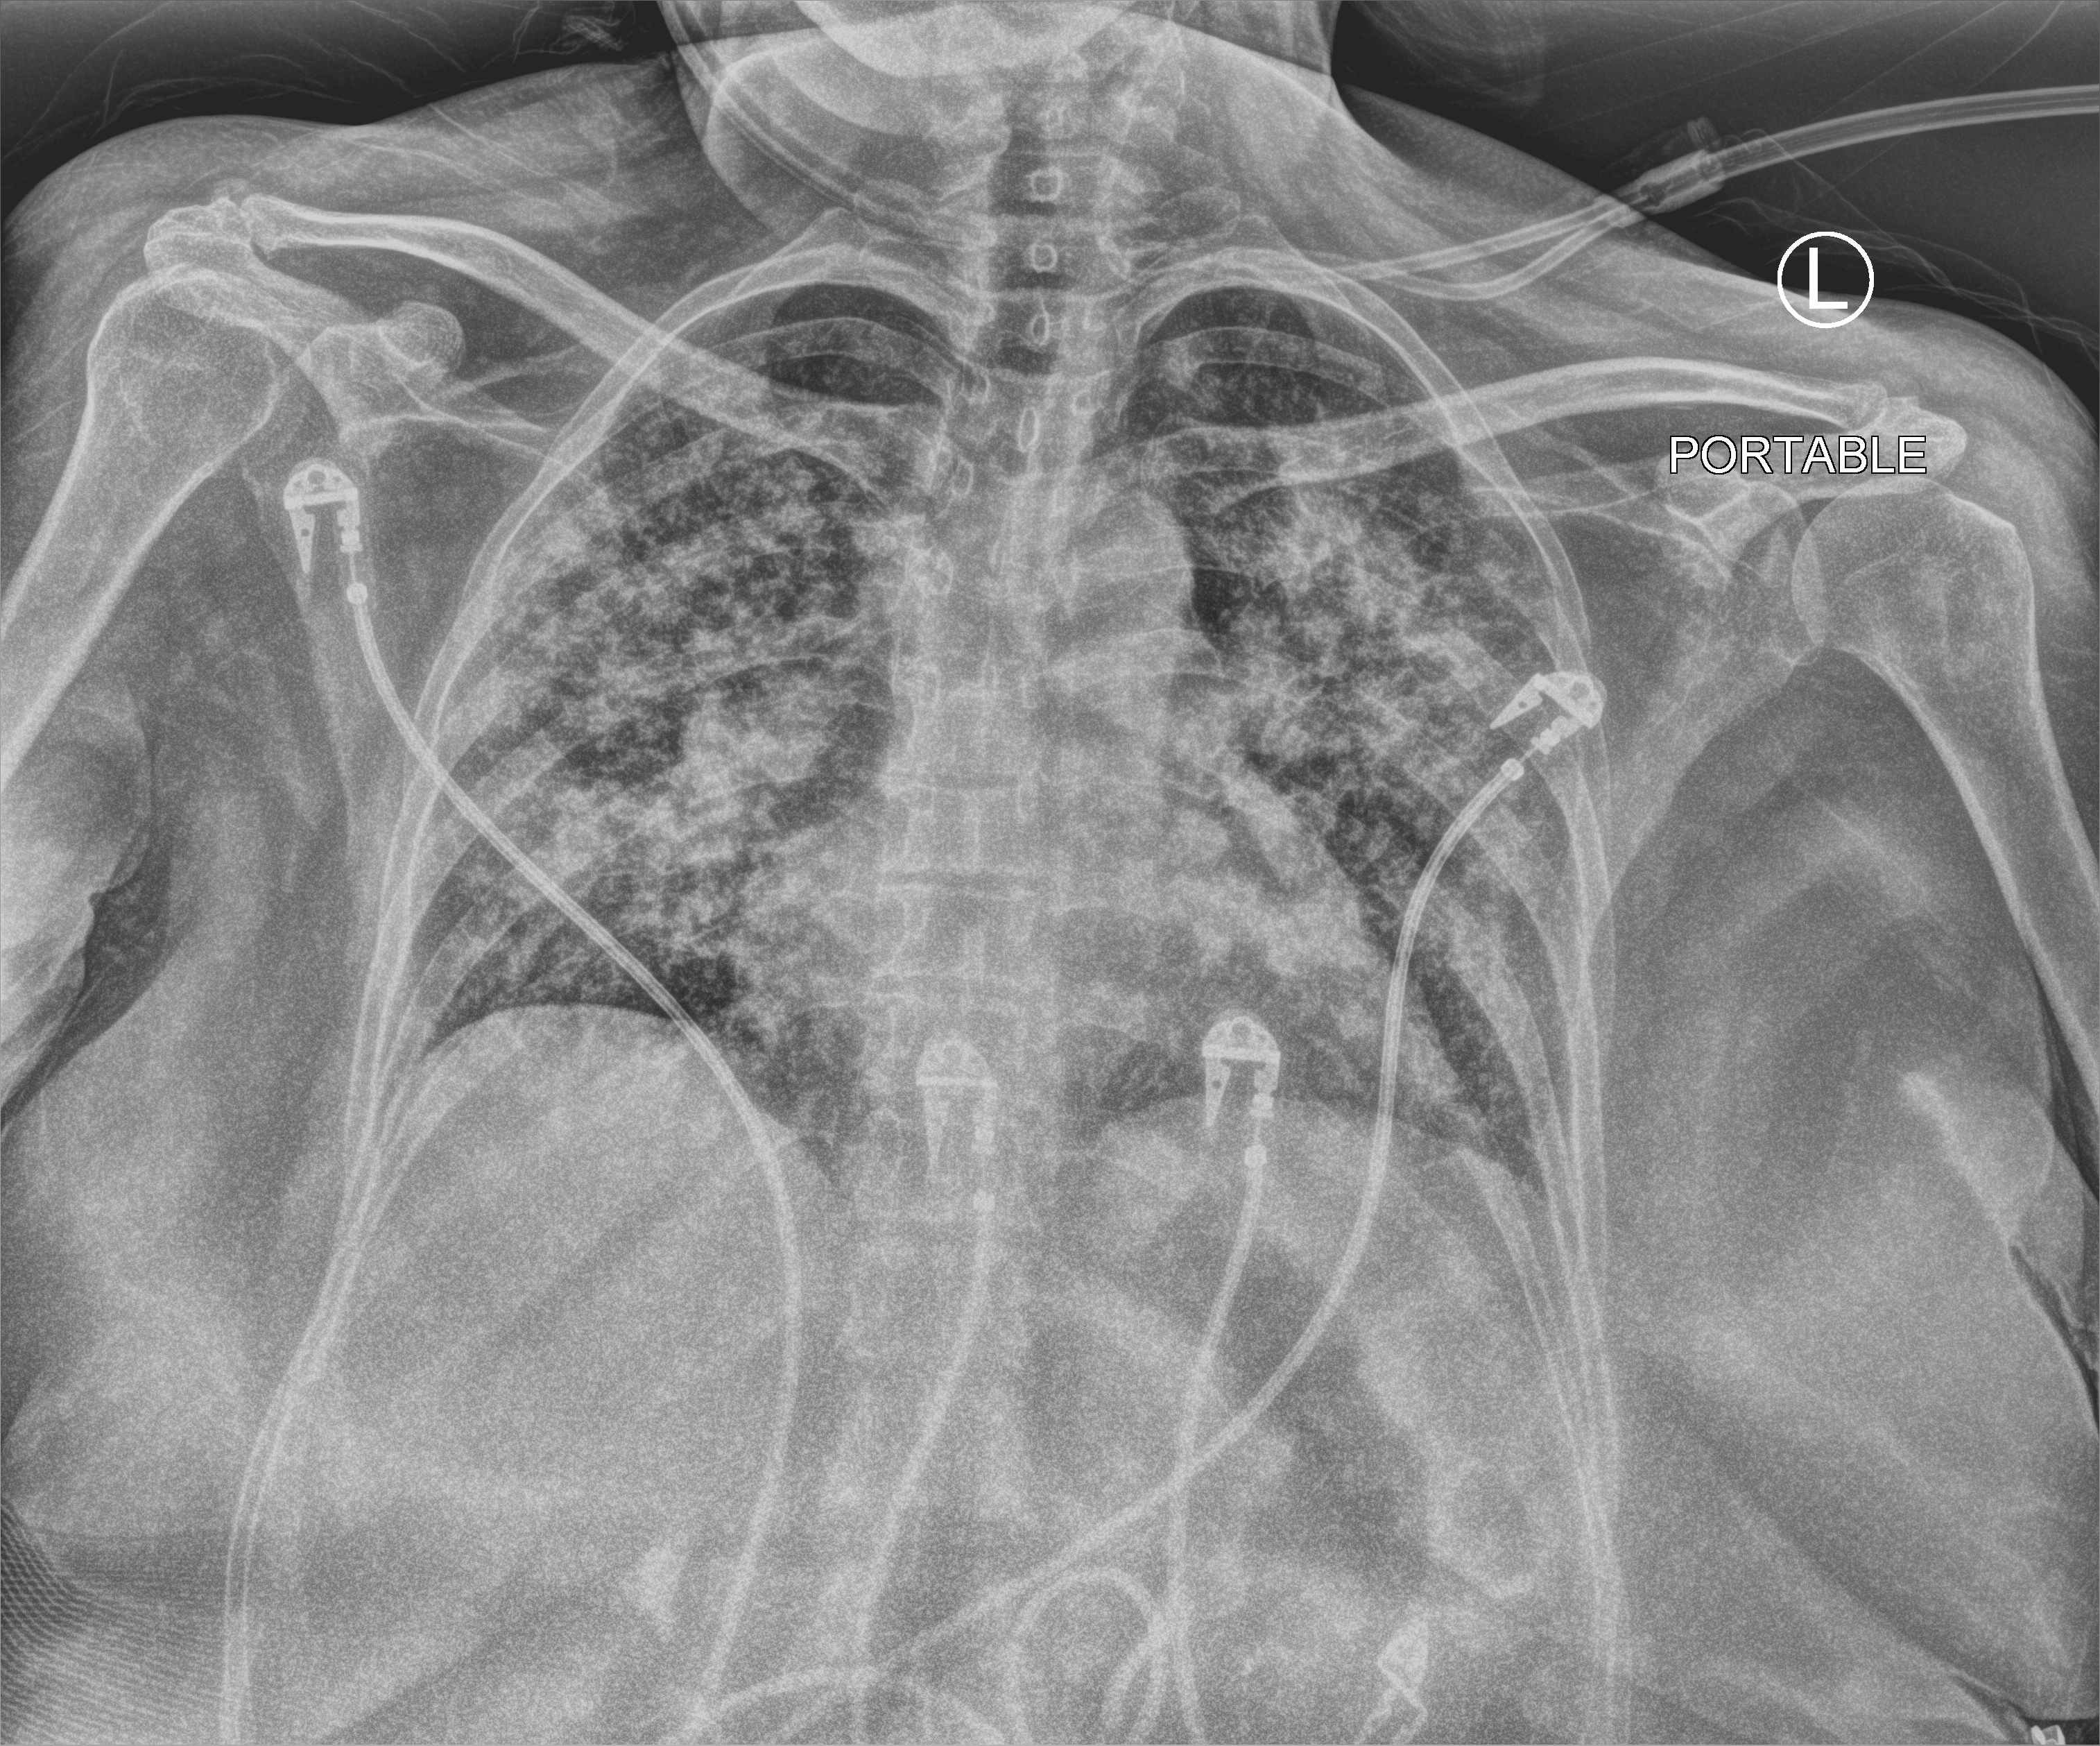
Chest X-ray (portable), anteroposterior (AP) projection. Female patient hospitalised with COVID-19, age 18–59 years.
Hospital-stay facts (about this admission, not read from this image; timing relative to this image not recorded): diabetes (admission record): no; COPD (admission record): no.